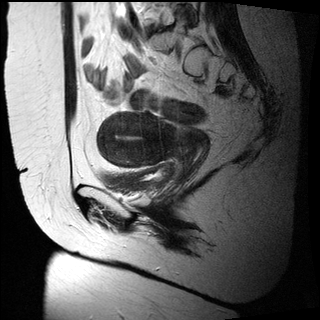
Pelvic MRI for cervical cancer, one sagittal slice; T2-weighted; 1.5 T; TE 89 ms, TR 2740 ms; 4 mm slice thickness; 320 × 320 image matrix, field of view 260 × 260 mm. Female patient, age 47 years.
Outlined on this slice (outlined manually by an expert reader):
- uterus and cervix: bounding box [x1, y1, x2, y2] px = [95, 113, 203, 168]